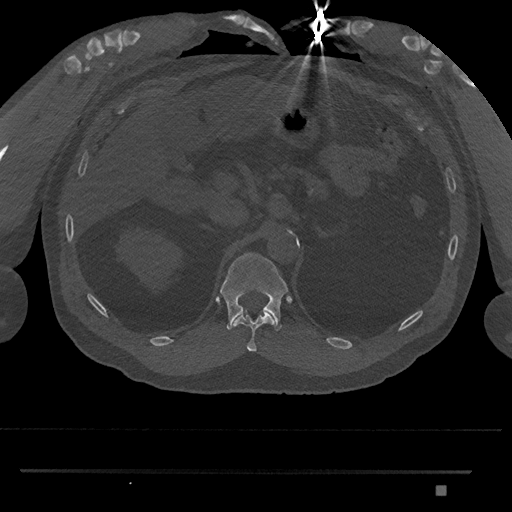
CT including the spine, one axial slice. Slice 912 of 1134 in the series (ordered by position). Reconstruction kernel Br40s/3. 120 kVp. Bone window (W 1800 / L 400 HU). 0.5 mm slice thickness. 512 × 512 image matrix. Patient: male, 65 years. Case-level facts recorded for this patient, not image findings: primary cancer: prostate.
Annotated regions visible in this slice (semi-automatically segmented with operator editing):
- T11 vertebra: box from (x=233, y=312) to (x=274, y=352) px
- T12 vertebra: (x=220, y=252)–(x=288, y=331)